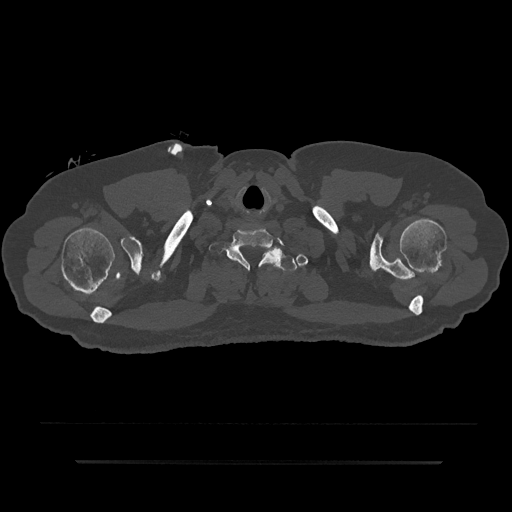
CT including the spine, one axial slice; position 763 of 797 along the scan axis; reconstruction kernel Br40s/3; bone window (W 1800 / L 400 HU); 0.5 mm slice thickness; 512 × 512 image matrix, field of view 464 × 464 mm. Patient: male, 59 years. From the clinical record (not read from this slice): primary cancer: bile ducts; vertebrae with lytic lesions (as recorded): T10.
Outlined on this slice (semi-automatic segmentation, software-assisted and operator-edited):
- T1 vertebra: bounding box <240,249,298,271> (left, top, right, bottom; pixels)